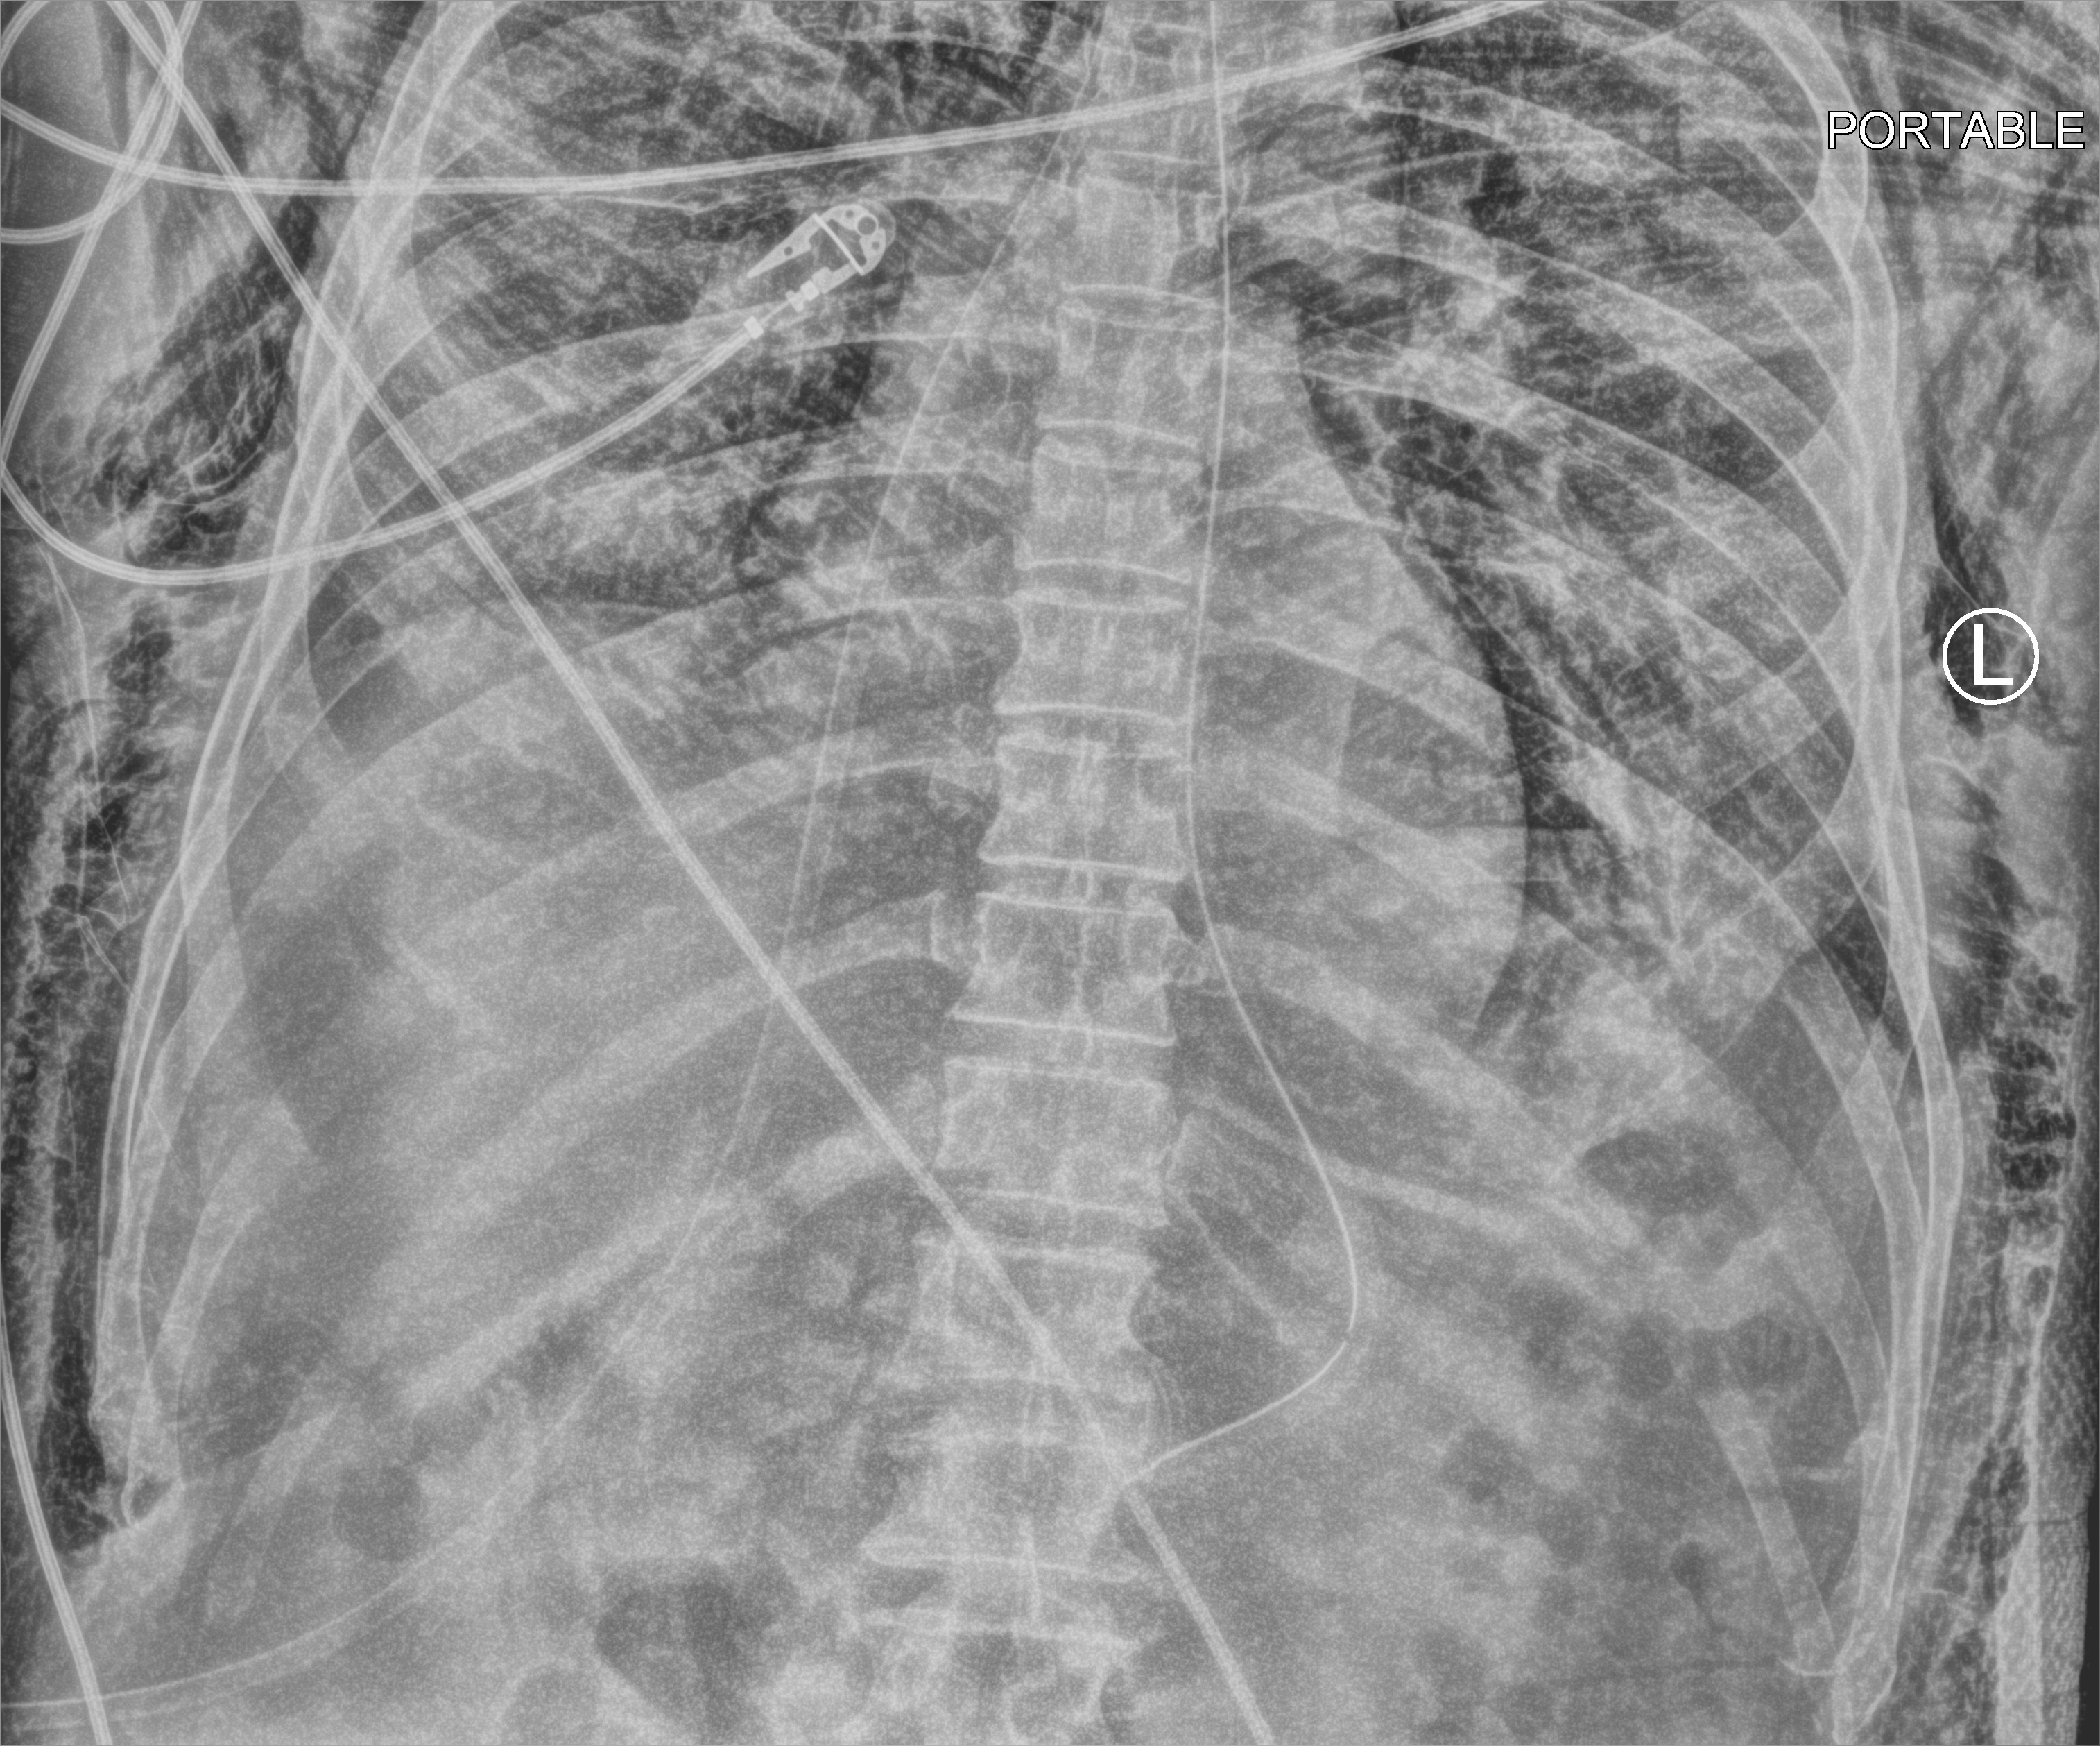
Portable chest radiograph; anteroposterior (AP) projection. Male patient hospitalised with COVID-19, age 60–74 years.
Hospital-stay facts (about this admission, not read from this image; timing relative to this image not recorded):
- other chronic lung disease (admission record): no
- chronic kidney disease (admission record): no
- mechanically ventilated during this hospital stay: yes